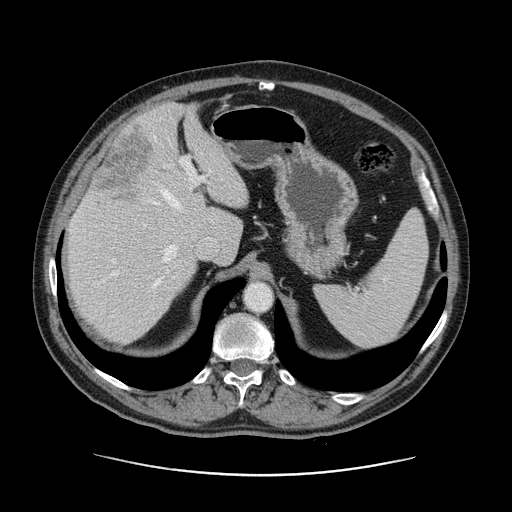
Contrast-enhanced abdominal CT, one axial slice. Position 90 of 141 along the scan axis. 120 kVp. Intravenous contrast given. Soft-tissue window (W 400 / L 40 HU). 512 × 512 image matrix, field of view 395 × 395 mm. Male patient, age 72 years. From the clinical record (not read from this slice): diagnosis: colorectal cancer liver metastases, imaged before liver resection; multiple liver metastases: yes; largest metastasis: 5.4 cm.
Outlined on this slice (outlined manually by an expert reader):
- hepatic veins: bounding box <153,183,180,288> (left, top, right, bottom; pixels)
- liver: <67,104,248,341>
- planned liver remnant (the part of the liver to remain after resection): <67,104,248,342>
- portal vein (with intrahepatic branches): <99,157,205,283>
- liver metastasis: <92,122,152,200>